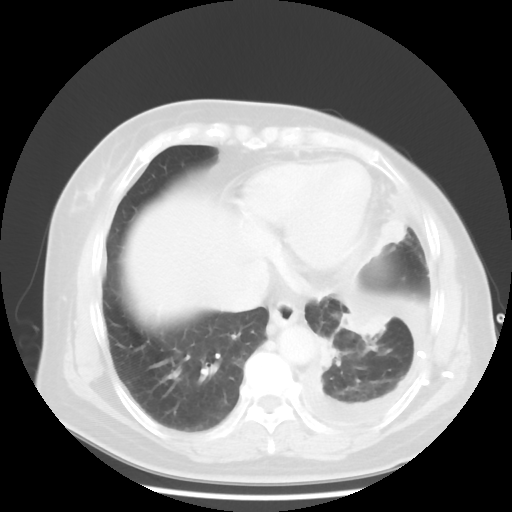
Chest CT, one axial slice. Position 13 of 48 along the scan axis. Reconstruction kernel STANDARD. Lung window (W 1500 / L -600 HU). 5 mm slice thickness. 512 × 512 image matrix, field of view 360 × 360 mm. Patient: female, 63 years. Case-level facts recorded for this patient, not image findings: clinical TNM (as recorded): T2 N0 M1.
Annotated regions visible in this slice (rectangle marked by the reading radiologist):
- lung tumour (recorded histology: adenocarcinoma): bounding box (x1, y1, x2, y2) in pixels: (334, 289, 395, 353)